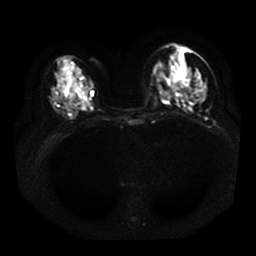
Breast MRI, one axial slice. Slice 16 of 41 in the series (ordered by position). Diffusion-weighted series; image 2 of 4 stored at this slice position (different b-values; order by instance number). 1.5 T. 5 mm slice thickness. 256 × 256 image matrix. Female patient.
Outlined on this slice (expert manual segmentation):
- tumour on diffusion-weighted imaging: bounding box <173,85,177,89> (left, top, right, bottom; pixels)